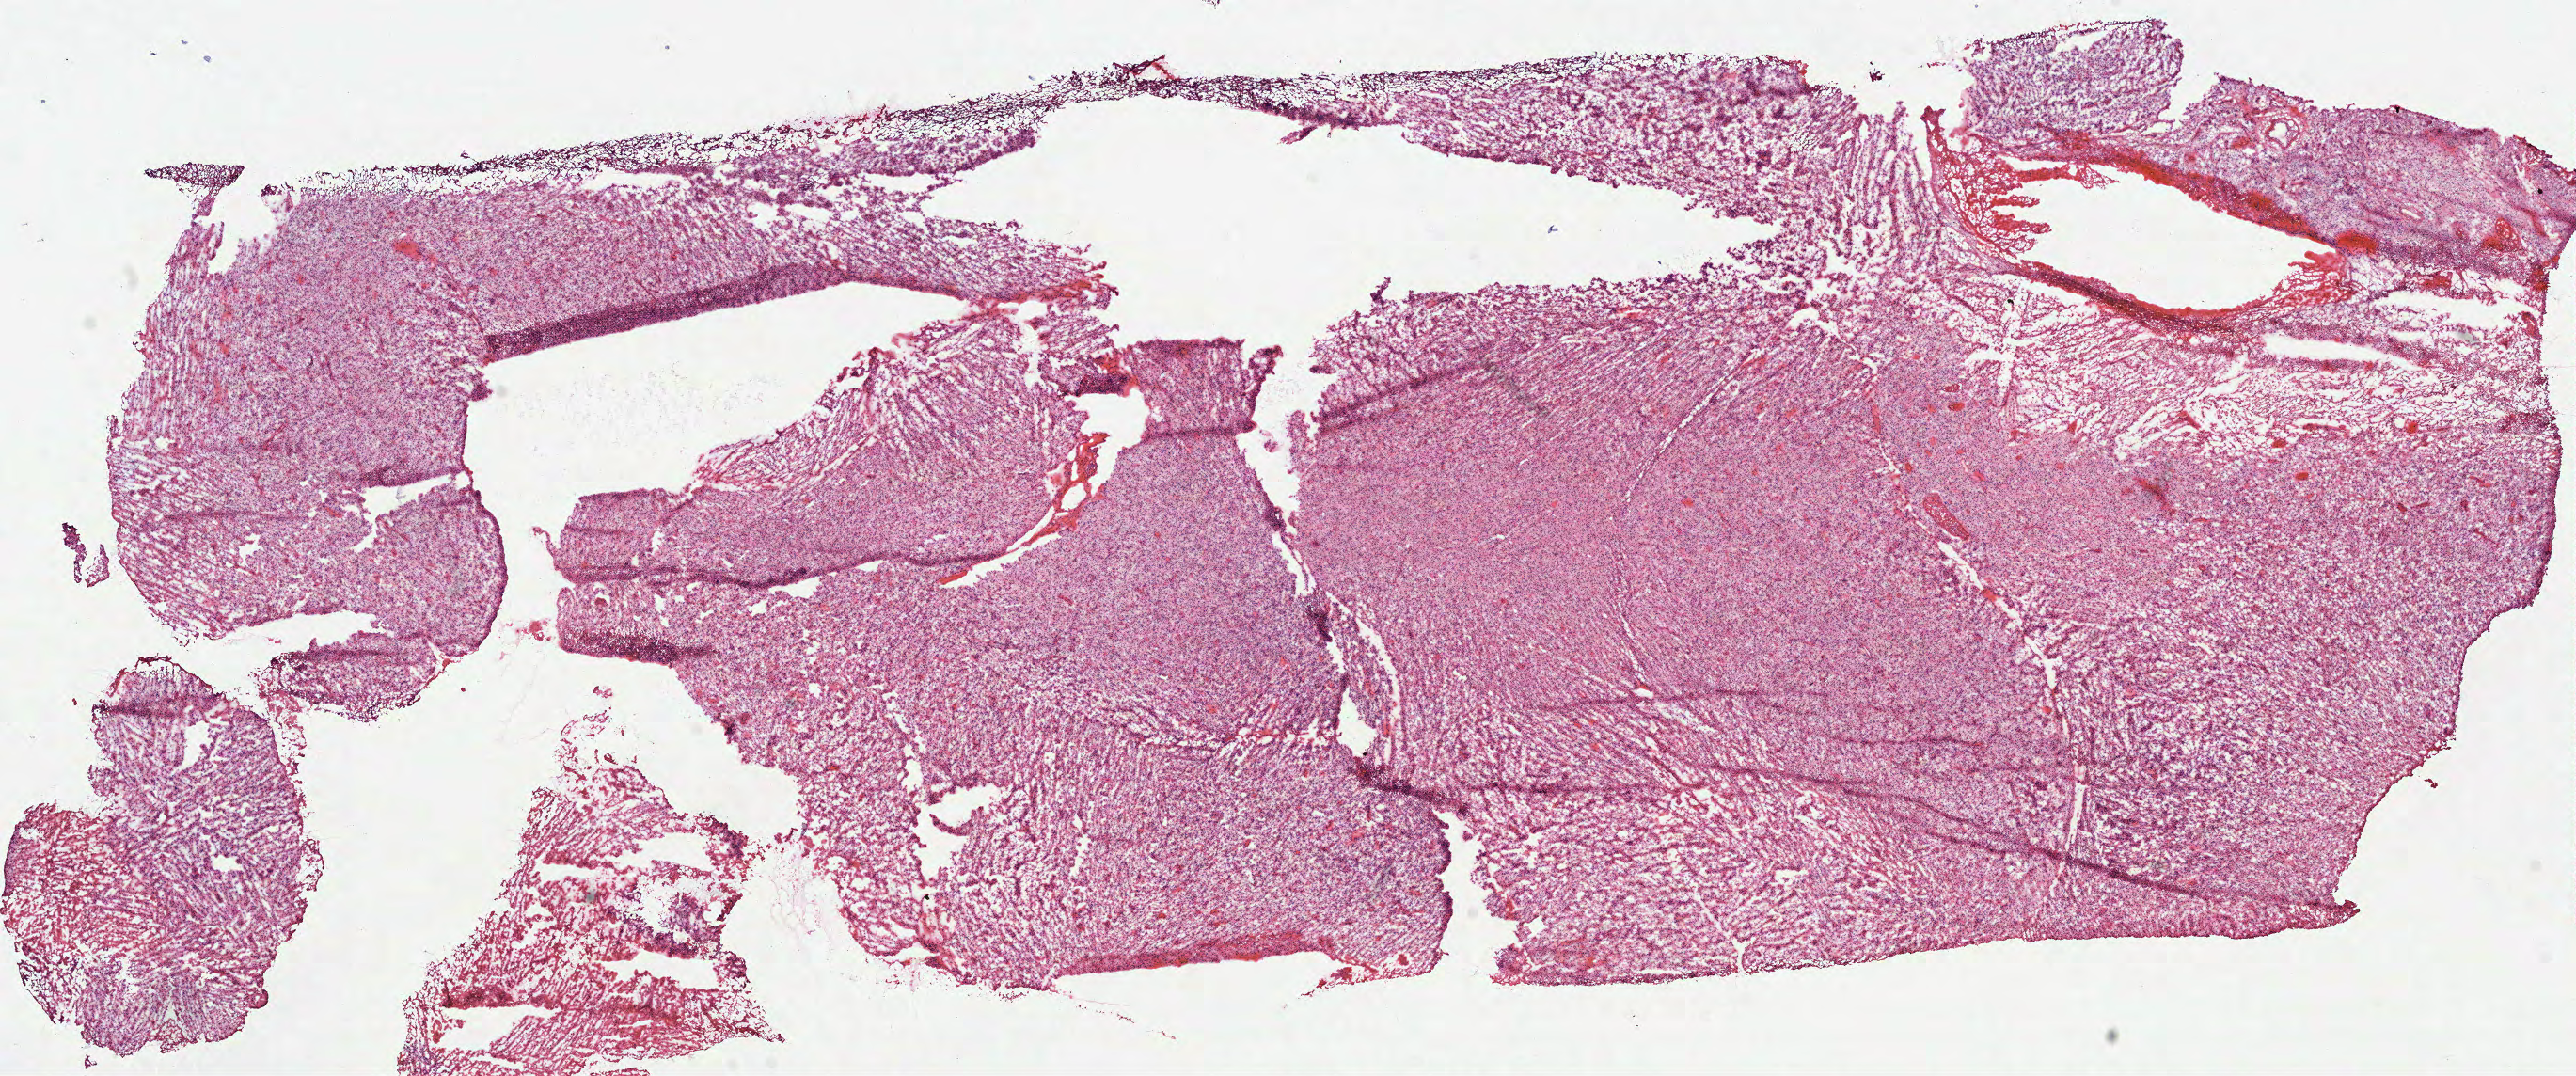
H&E-stained whole-slide image, a low-resolution overview of the entire scanned area, about 22.1 x 9.2 mm (slide scanned at 40x); frozen section from the top of the tissue portion; primary tumour sample from the brain. Male, age 66 years at initial diagnosis. Pathologist review of this section (percent, as recorded): tumour cells 100%, tumour nuclei 80%, normal cells 0%, stromal cells 0%, necrosis 0%.
Diagnosis: Glioblastoma.